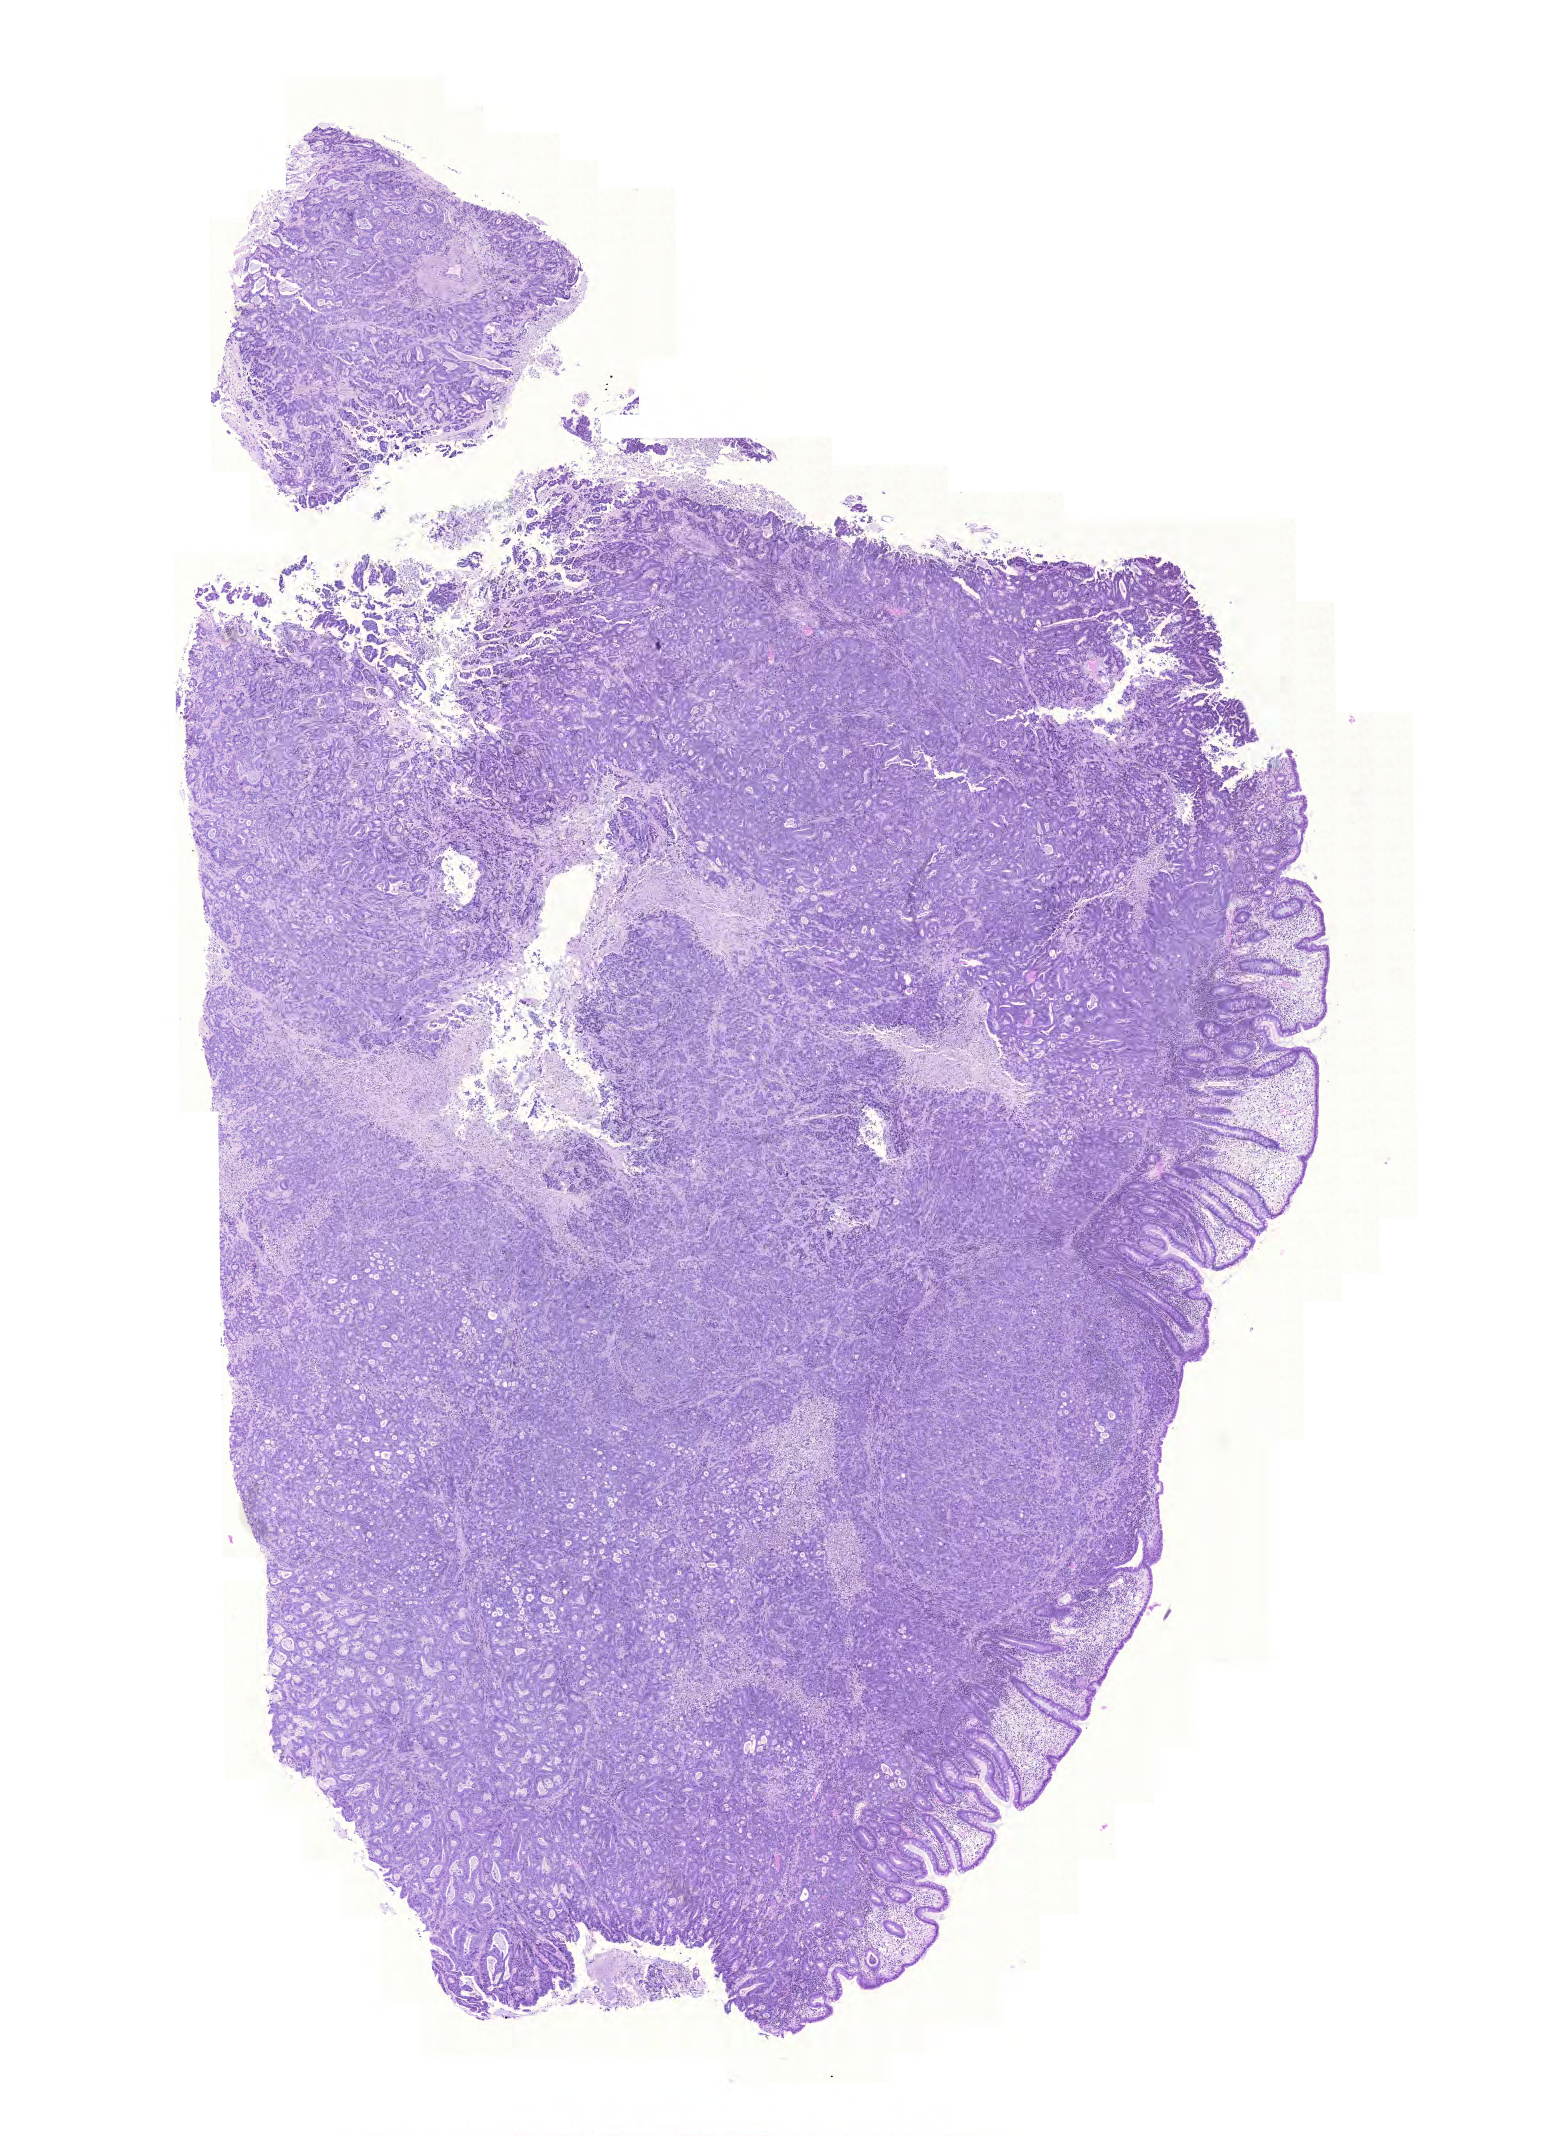
Whole-slide histology image, Hematoxylin and eosin (H&E) stained, low-resolution overview of the scanned area, about 11.6 x 15.9 mm, formalin-fixed paraffin-embedded (FFPE) diagnostic section, sample: primary tumour, colon. Female, age 81 years at initial diagnosis.
Diagnosis: Adenocarcinoma, NOS (cecum). AJCC pathologic stage: IIA (6th edition).